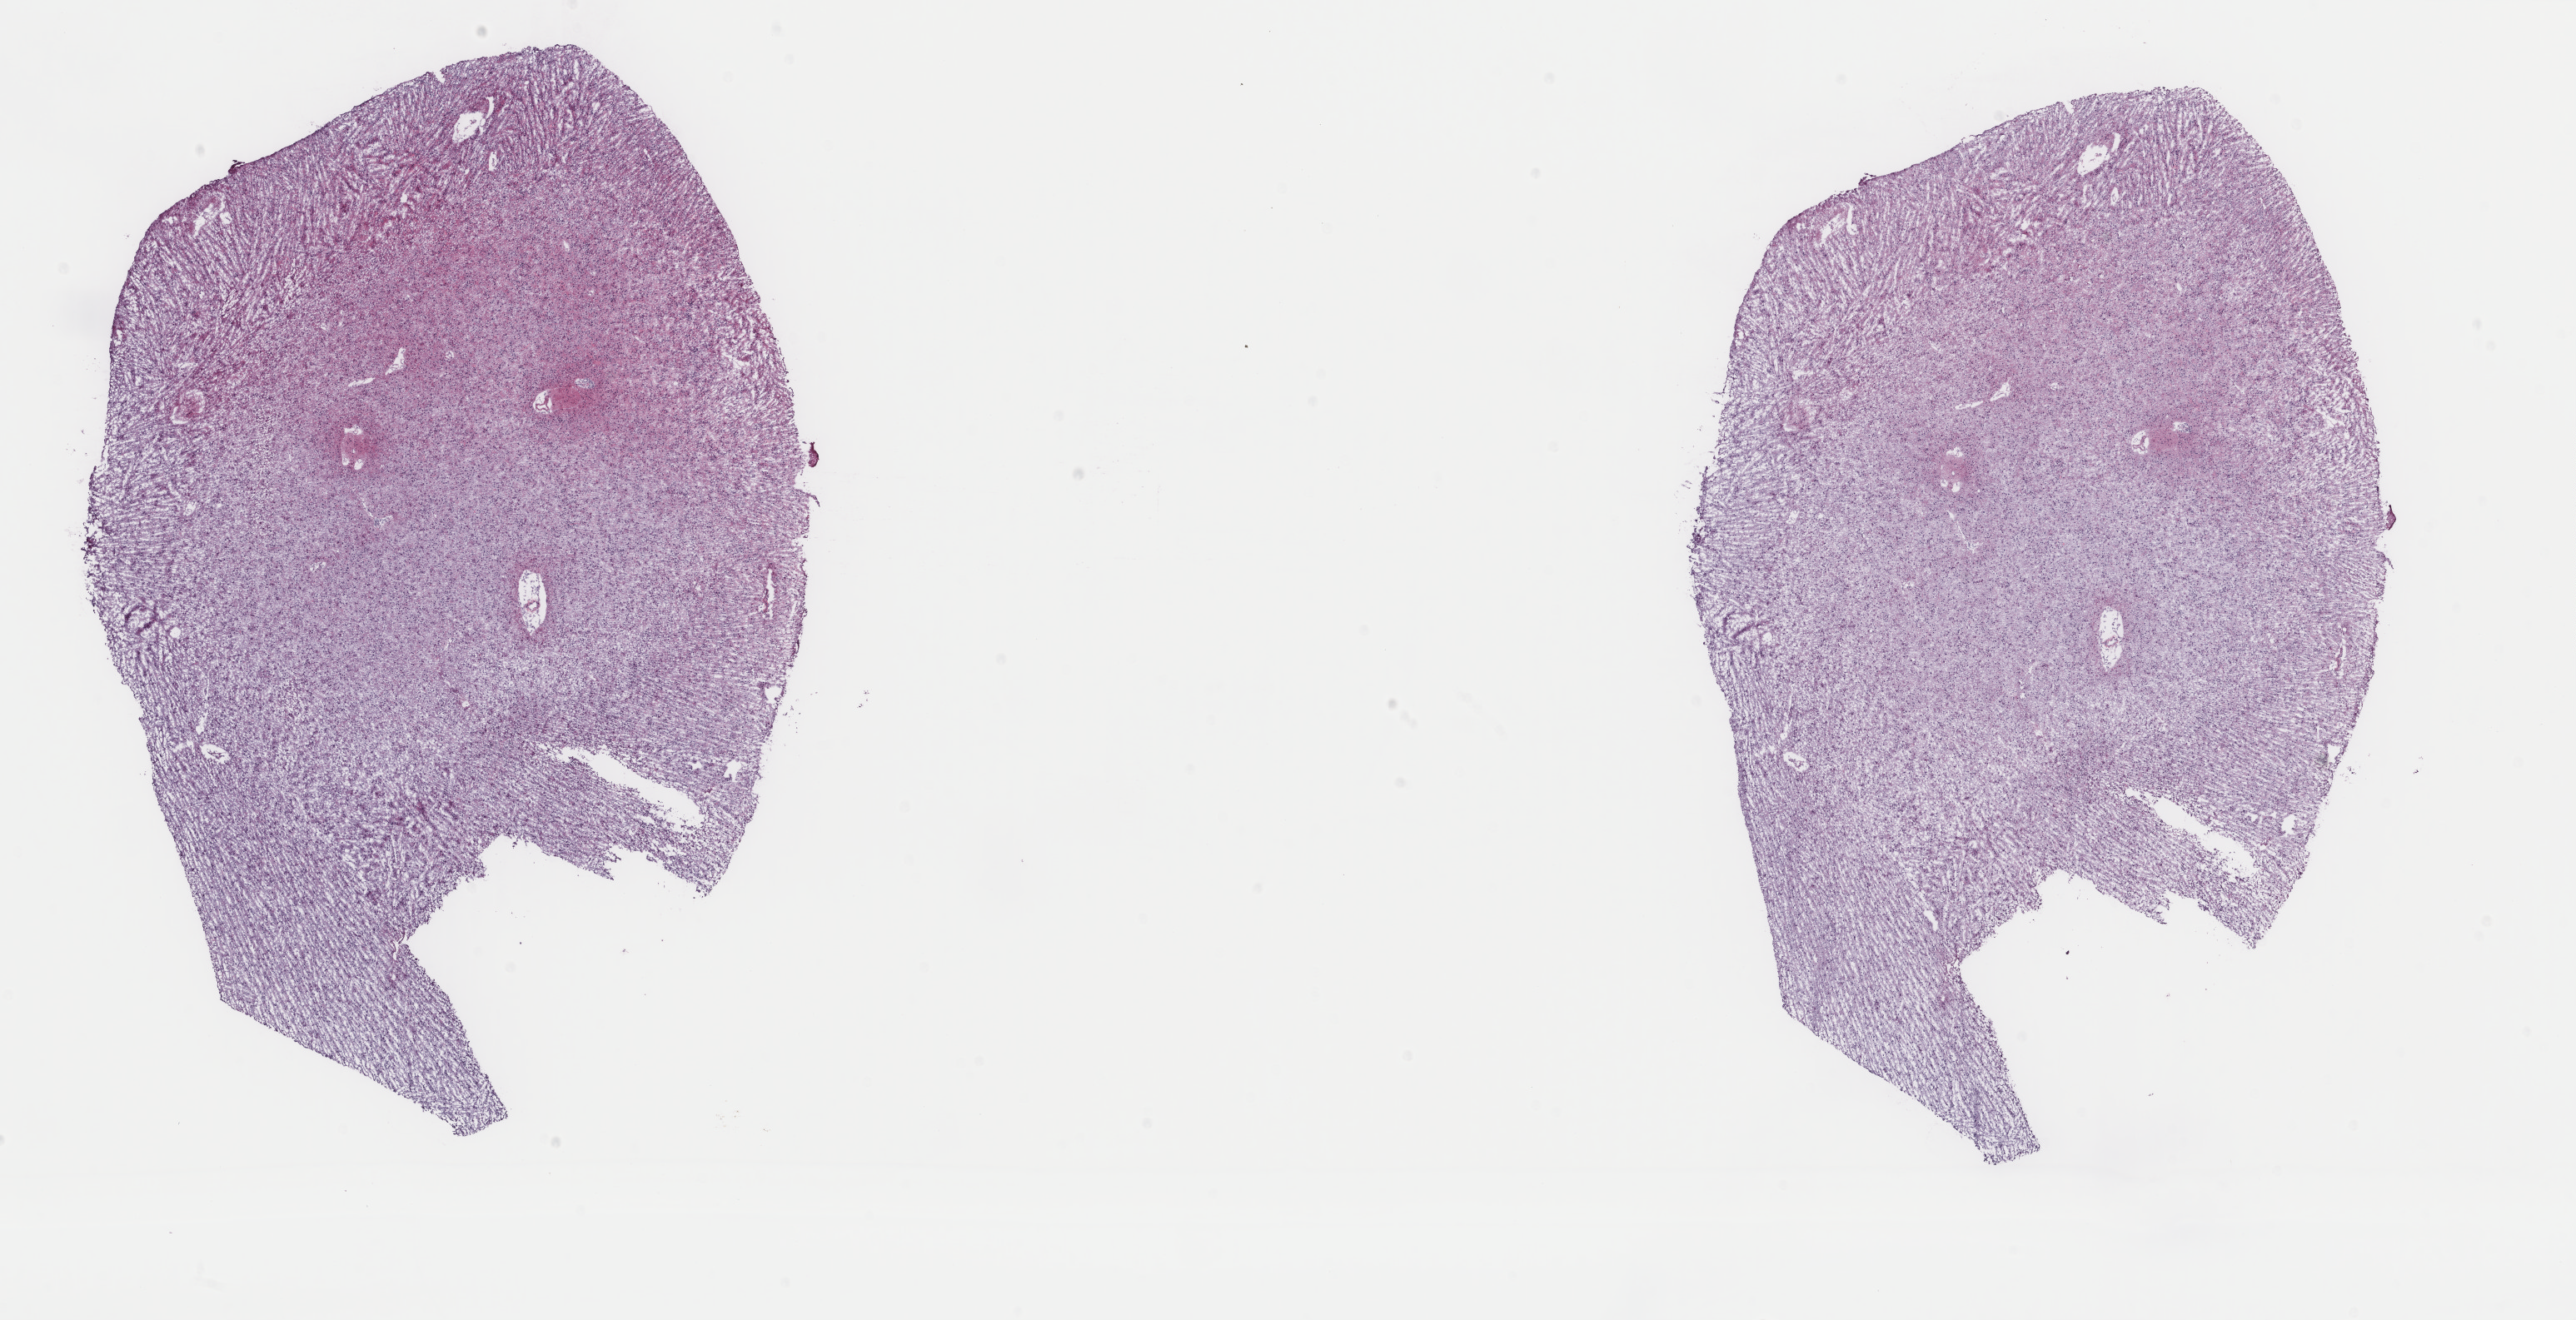
Hematoxylin and eosin (H&E) stained whole-slide image, shown as a low-resolution overview of the whole scanned area (about 24.6 x 12.6 mm); frozen section from the top of the tissue portion; sample: primary tumour, brain. Female patient; age at initial diagnosis 47 years. Pathologist review of this section (percent, as recorded): tumour cells 60%, tumour nuclei 90%.
Pathologic diagnosis: Mixed glioma (cerebrum).